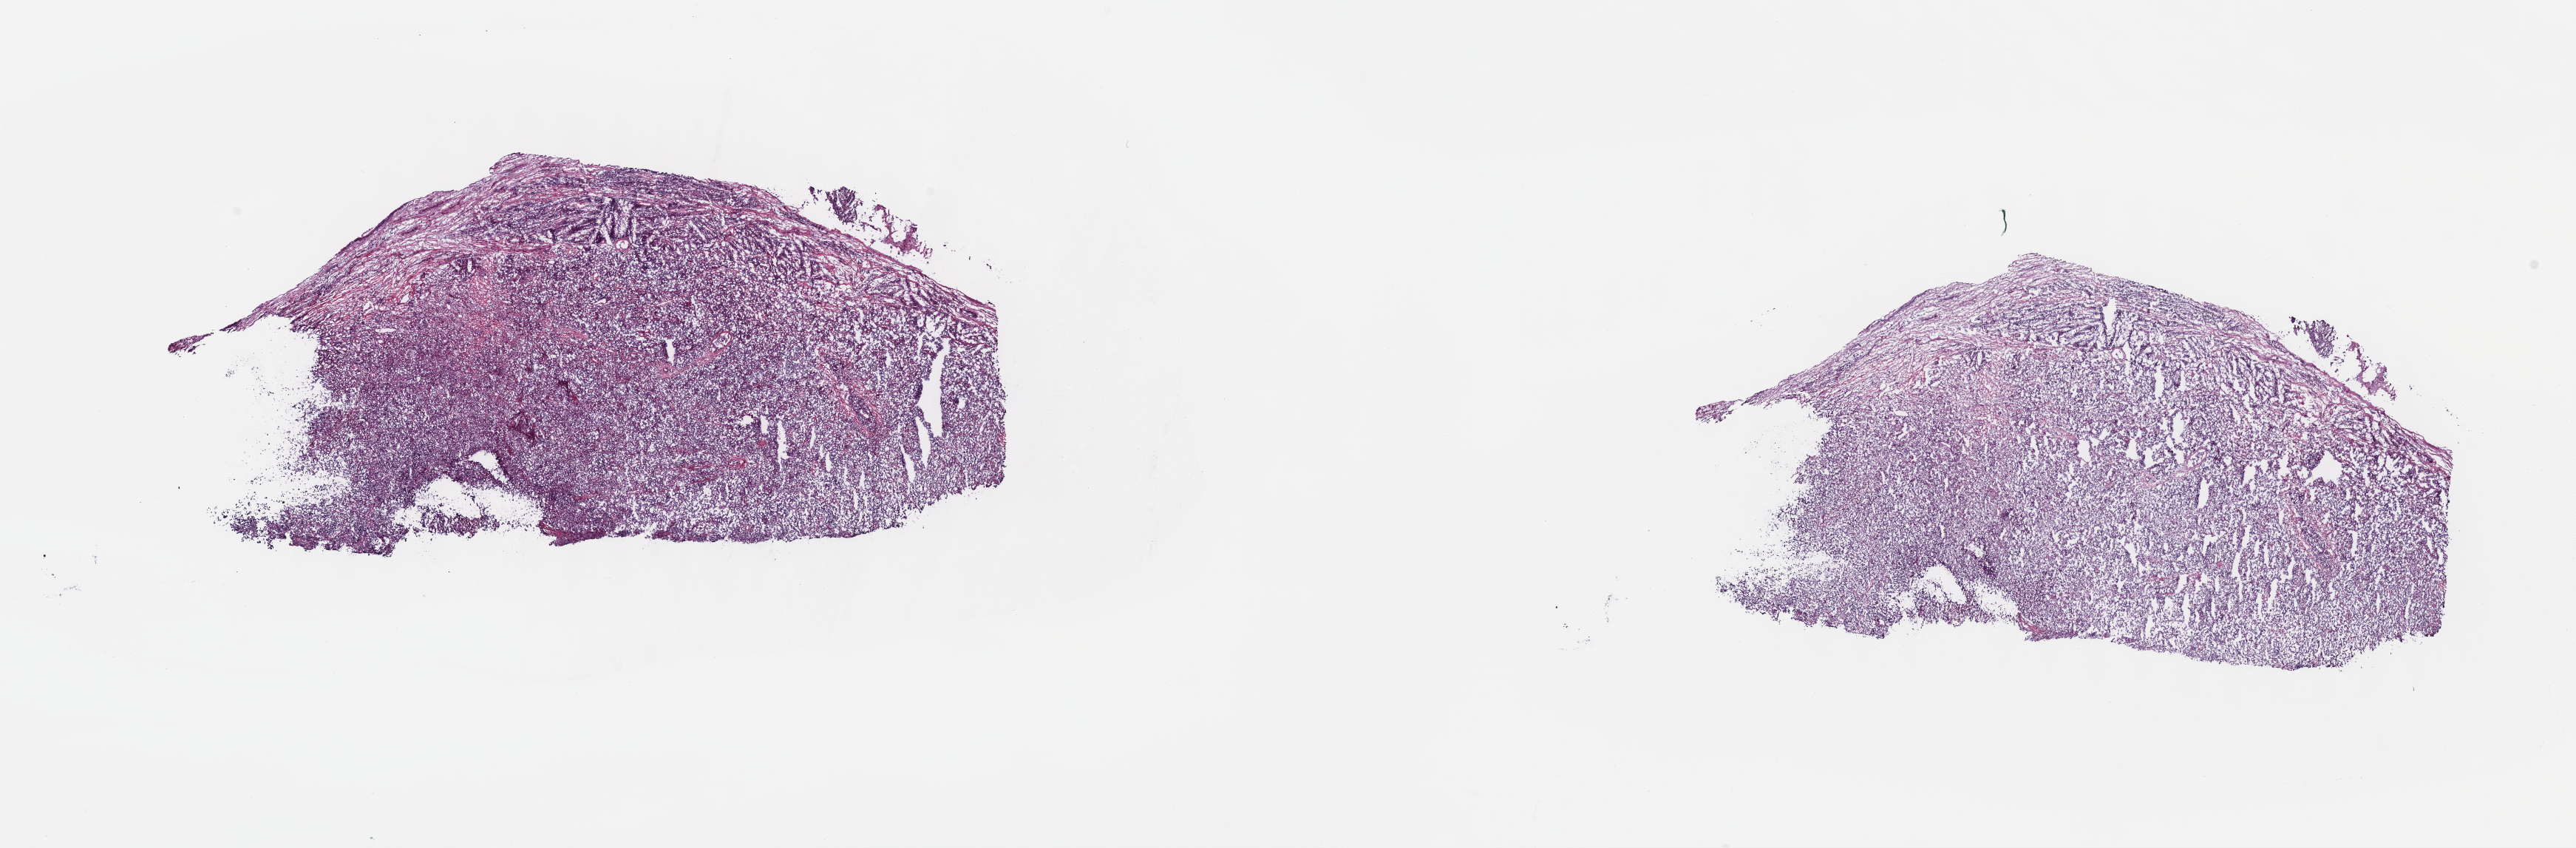
H&E whole-slide image — low-resolution overview of the scanned area, about 28.2 x 9.3 mm; frozen section from the top of the tissue portion; testis, primary tumour sample. Patient: male, age at initial diagnosis 31 years. Composition of this section per pathologist review: tumour cells 80%, tumour nuclei 90%, normal cells 0%, stromal cells 20%, necrosis 0%. Infiltration values recorded for this section: lymphocyte infiltration 0%, monocyte infiltration 0%, neutrophil infiltration 0%.
AJCC pathologic stage: IA (7th edition). Histologic diagnosis: Seminoma, NOS. Laterality: right.